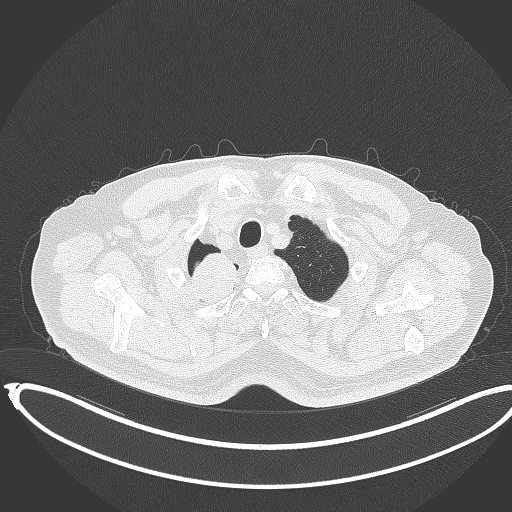
Chest CT, one axial slice. Position 335 of 403 along the scan axis. Reconstruction kernel B70f. Lung window (W 1500 / L -600 HU). 512 × 512 image matrix. Patient: male, 68 years. Case-level facts recorded for this patient, not image findings: clinical TNM (as recorded): T2a N0 M0.
Annotated regions visible in this slice (rectangle marked by the reading radiologist):
- lung tumour (recorded histology: adenocarcinoma): box from (x=180, y=246) to (x=245, y=307) px